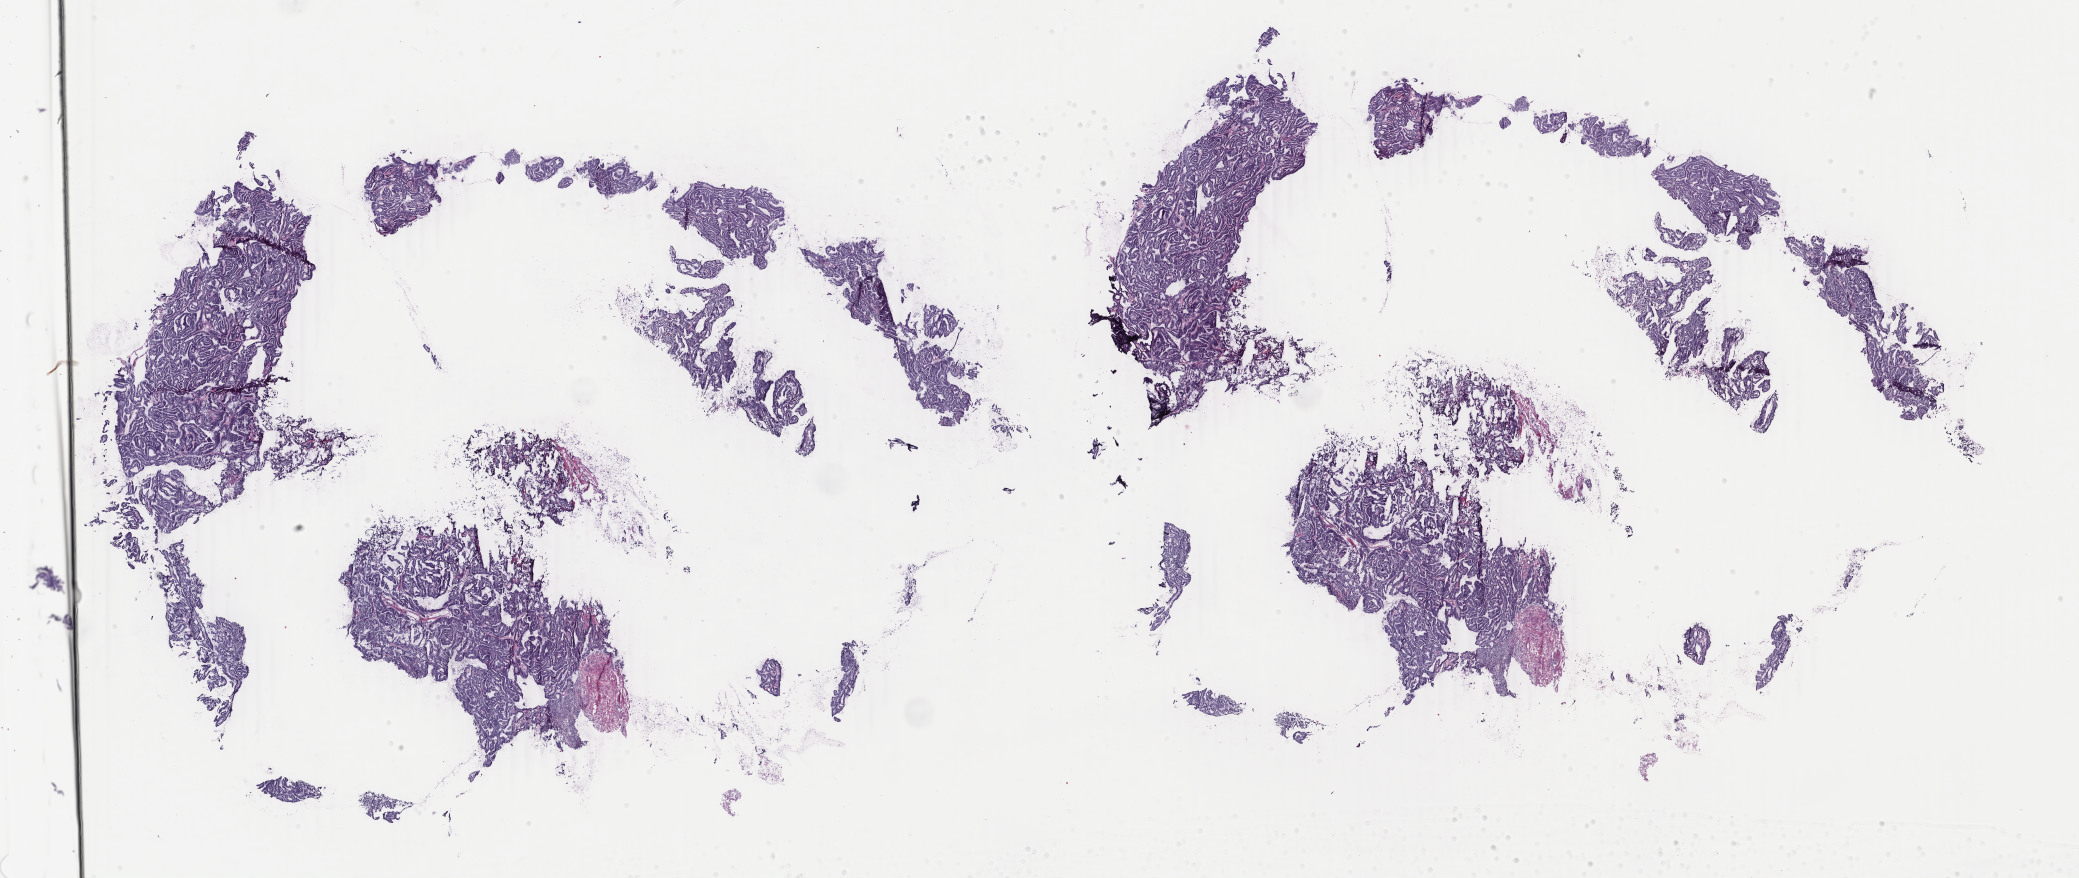
Whole-slide histology image, H&E-stained, a low-resolution overview of the entire scanned area, about 33.1 x 14.0 mm (acquisition: 40x scan); frozen section from the bottom of the tissue portion; sample: primary tumour, uterus. Patient: female, age at initial diagnosis 63 years. Histologic grade: G1 (well differentiated). Composition of this section per pathologist review: tumour cells 90%, tumour nuclei 96%, normal cells 0%, stromal cells 6%, necrosis 4%. Inflammatory infiltration, as recorded: lymphocyte infiltration 2%, monocyte infiltration 0%, neutrophil infiltration 0%.
* pathologic diagnosis: Endometrioid adenocarcinoma, NOS (endometrium)
* FIGO stage: IA